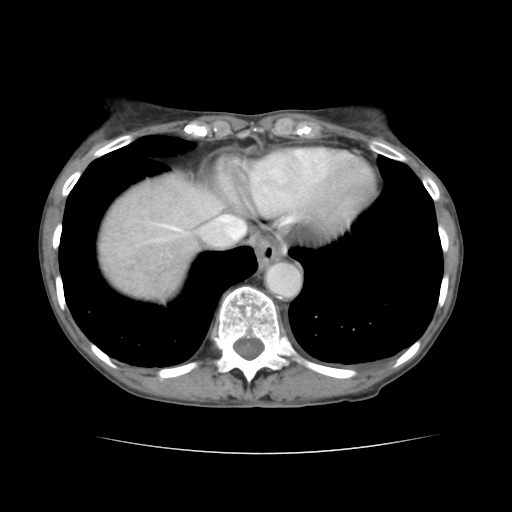
Contrast-enhanced abdominal CT, one axial slice. Position 128 of 136 along the scan axis. 120 kVp. Intravenous contrast given. Soft-tissue window (W 400 / L 40 HU). 2.5 mm slice thickness. 512 × 512 image matrix. Female patient, age 77 years. From the clinical record (not read from this slice): diagnosis: colorectal cancer liver metastases, imaged before liver resection; multiple liver metastases: yes; largest metastasis: 3 cm; chemotherapy before resection: yes.
Structures marked on this image (outlined manually by an expert reader):
- hepatic veins: box from (x=149, y=201) to (x=246, y=246) px
- liver: (x=98, y=175)–(x=221, y=299)
- planned liver remnant (the part of the liver to remain after resection): (x=201, y=189)–(x=221, y=213)